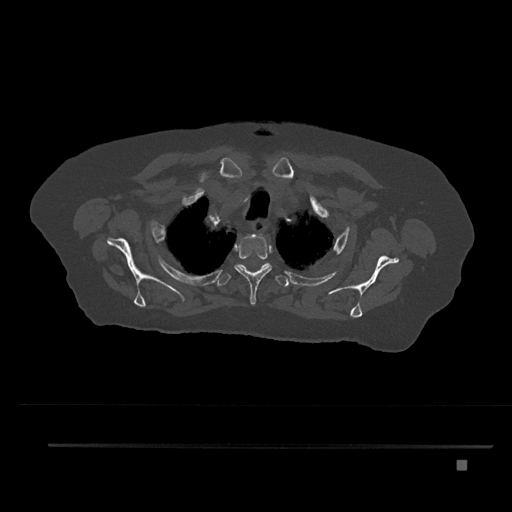
CT including the spine, one axial slice; bone window (W 1800 / L 400 HU); 0.5 mm slice thickness; 512 × 512 image matrix, field of view 437 × 437 mm. Patient: female, 76 years. From the clinical record (not read from this slice): primary cancer: lung.
Outlined on this slice (semi-automatically segmented with operator editing):
- T1 vertebra: bounding box <252,233,256,237> (left, top, right, bottom; pixels)
- T2 vertebra: <234,235,272,305>
- T3 vertebra: <217,263,289,287>